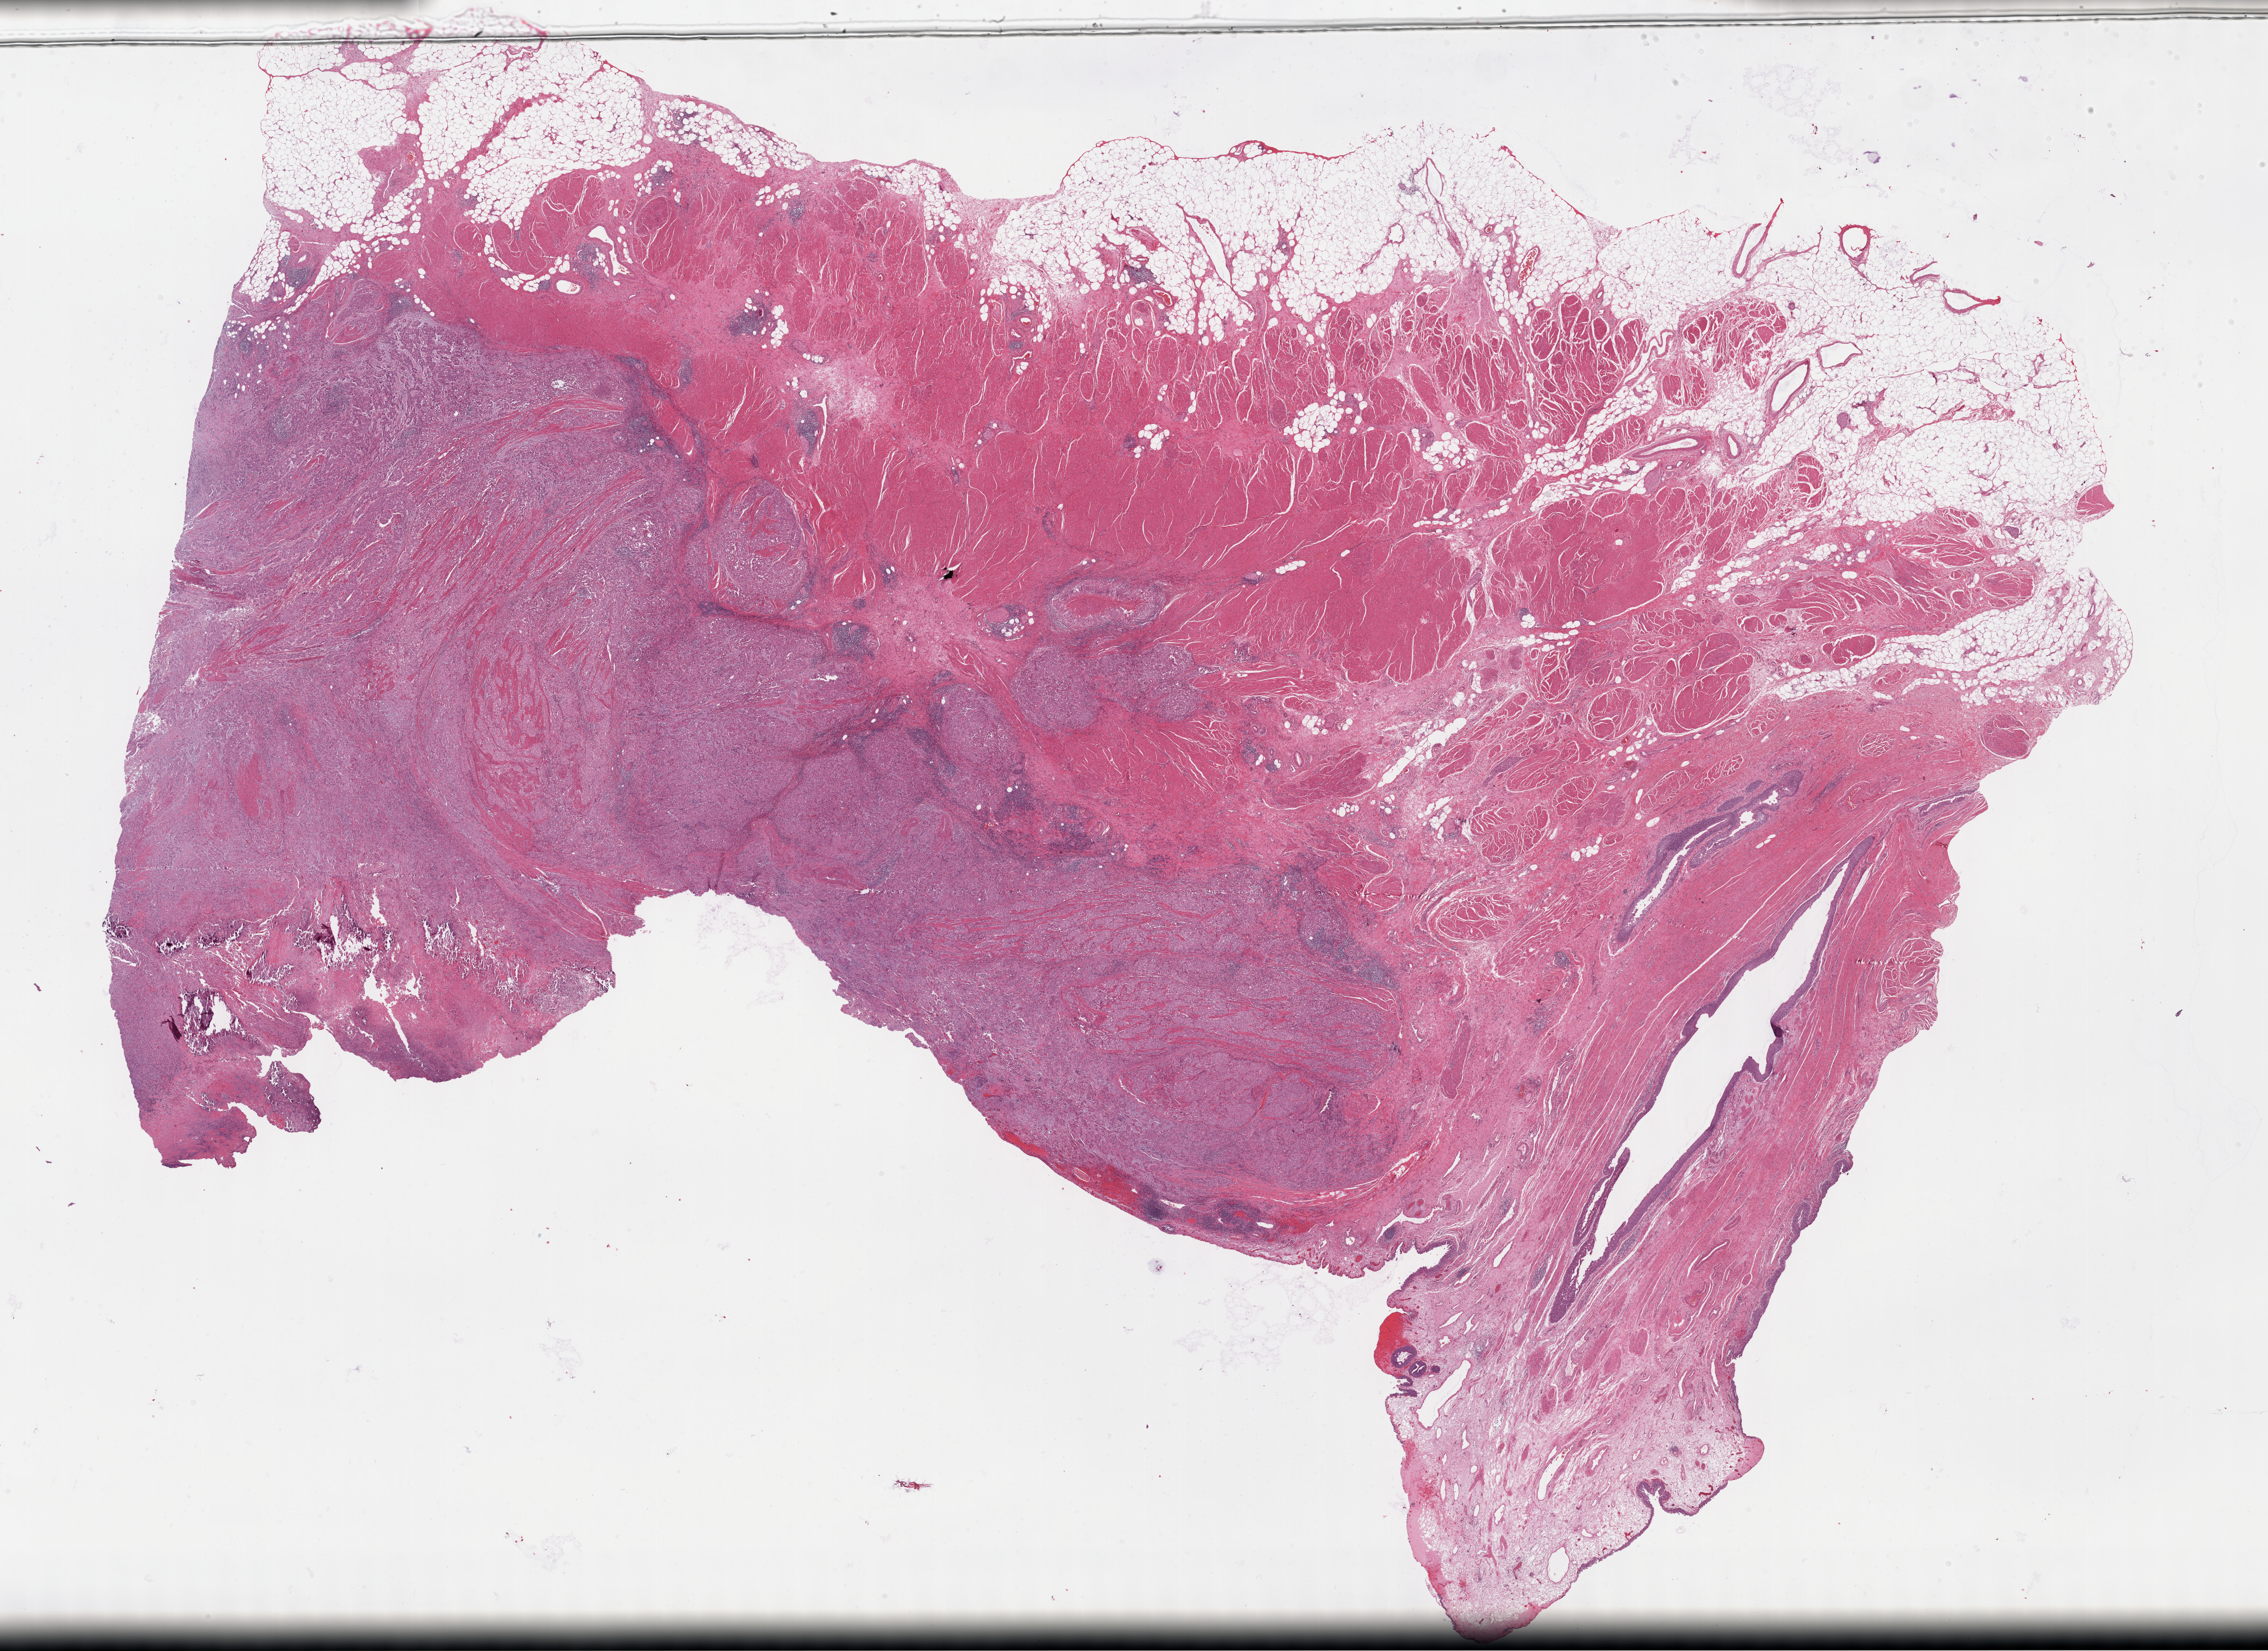
Whole-slide histology image, H&E-stained, shown as a low-resolution overview of the whole scanned area (about 32.7 x 23.8 mm, acquisition: 40x scan), FFPE section, sample: primary tumour, bladder. Male, age 58 years at initial diagnosis. Histologic grade: high grade.
- AJCC pathologic stage: IV (7th edition)
- histologic diagnosis: Papillary transitional cell carcinoma (lateral wall of bladder)